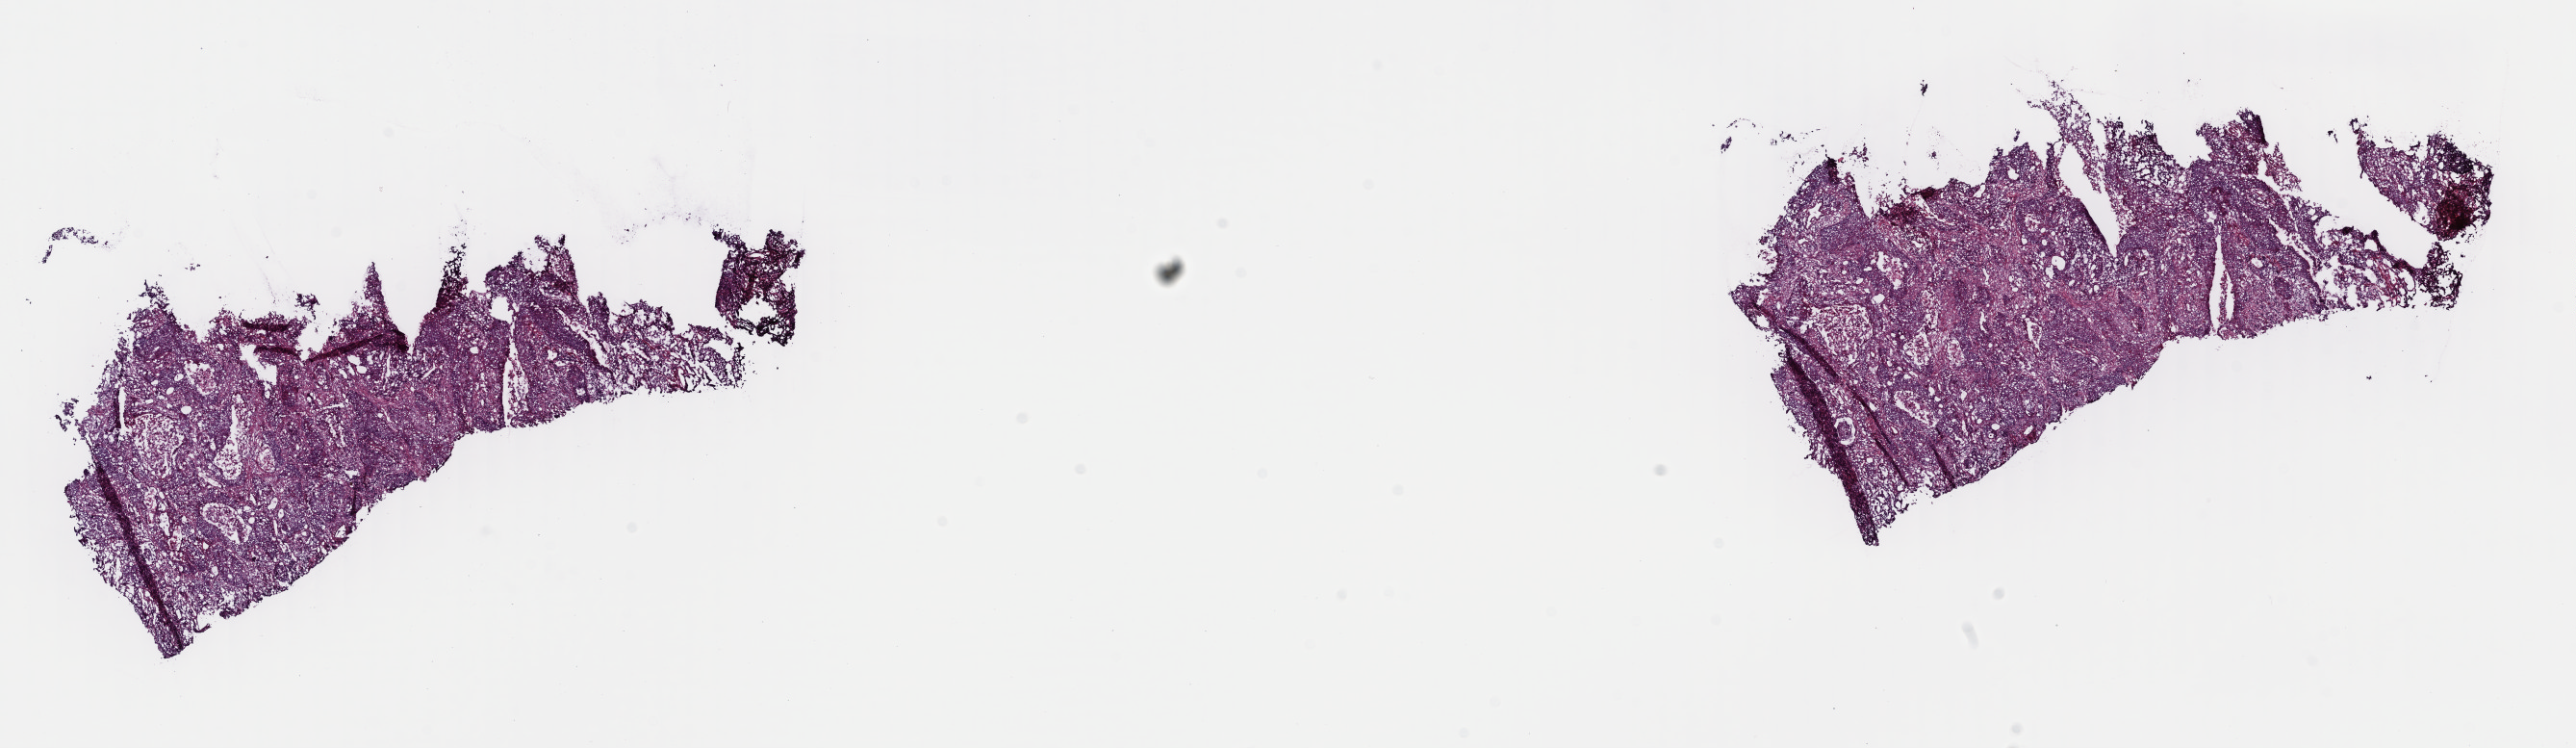
H&E whole-slide image — whole scanned area (about 21.1 x 6.1 mm) shown as a low-resolution overview, frozen section from the top of the tissue portion, lung, primary tumour sample. Male patient; age at initial diagnosis 73 years. Slide review estimates, as recorded: tumour cells 75%, tumour nuclei 80%, normal cells 0%, stromal cells 20%, necrosis 5%. Inflammatory infiltration, as recorded: lymphocyte infiltration 5%, monocyte infiltration 0%, neutrophil infiltration 0%.
AJCC pathologic stage: IIA. Histologic diagnosis: Squamous cell carcinoma, NOS (lower lobe, lung). TNM: T2b N0 MX.